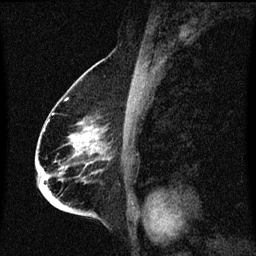
Breast MRI (dynamic contrast-enhanced), one sagittal slice; slice 39 of 60 in the series (ordered by position); dynamic contrast-enhanced series, image 2 of 3 at this slice position (ordered by acquisition); 1.5 T; TE 4.2 ms, TR 8.4 ms; 256 × 256 image matrix. Patient: female, 68 years. From the clinical record (not read from this slice): setting: breast cancer imaged before/during neoadjuvant chemotherapy; receptor status: triple-negative.
Annotated regions visible in this slice (semi-automatic segmentation, software-assisted and operator-edited):
- analysis volume of interest (the breast-tissue region the enhancement analysis was run in; not a lesion): bounding box <37,96,113,213> (left, top, right, bottom; pixels)
- tumour enhancement mask (voxels above the 70 % enhancement threshold inside the analysis volume of interest): <75,132,100,151>